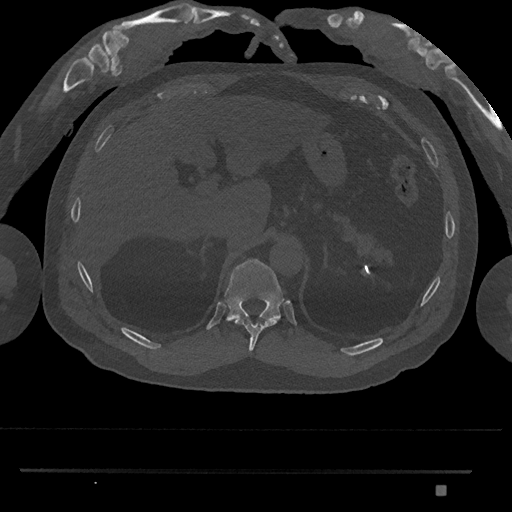
CT including the spine, one axial slice; slice 970 of 1134 in the series (ordered by position); reconstruction kernel Br40s/3; 120 kVp; bone window (W 1800 / L 400 HU); 512 × 512 image matrix, field of view 429 × 429 mm. Male patient, age 65 years. Case-level facts recorded for this patient, not image findings: primary cancer: prostate.
Outlined on this slice (semi-automatically segmented with operator editing):
- T10 vertebra: bounding box <235,318,276,354> (left, top, right, bottom; pixels)
- T11 vertebra: <223,259,285,334>